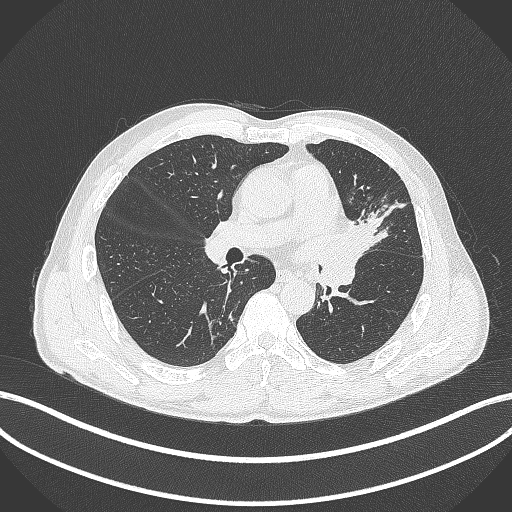
Chest CT, one axial slice. Position 231 of 429 along the scan axis. 120 kVp. Lung window (W 1500 / L -600 HU). 1 mm slice thickness. 512 × 512 image matrix, field of view 400 × 400 mm. Male patient, age 57 years. From the clinical record (not read from this slice): clinical TNM (as recorded): T2b N0 M0.
Annotated regions visible in this slice (rectangle marked by the reading radiologist):
- lung tumour (recorded histology: squamous cell carcinoma): box from (x=337, y=205) to (x=382, y=279) px